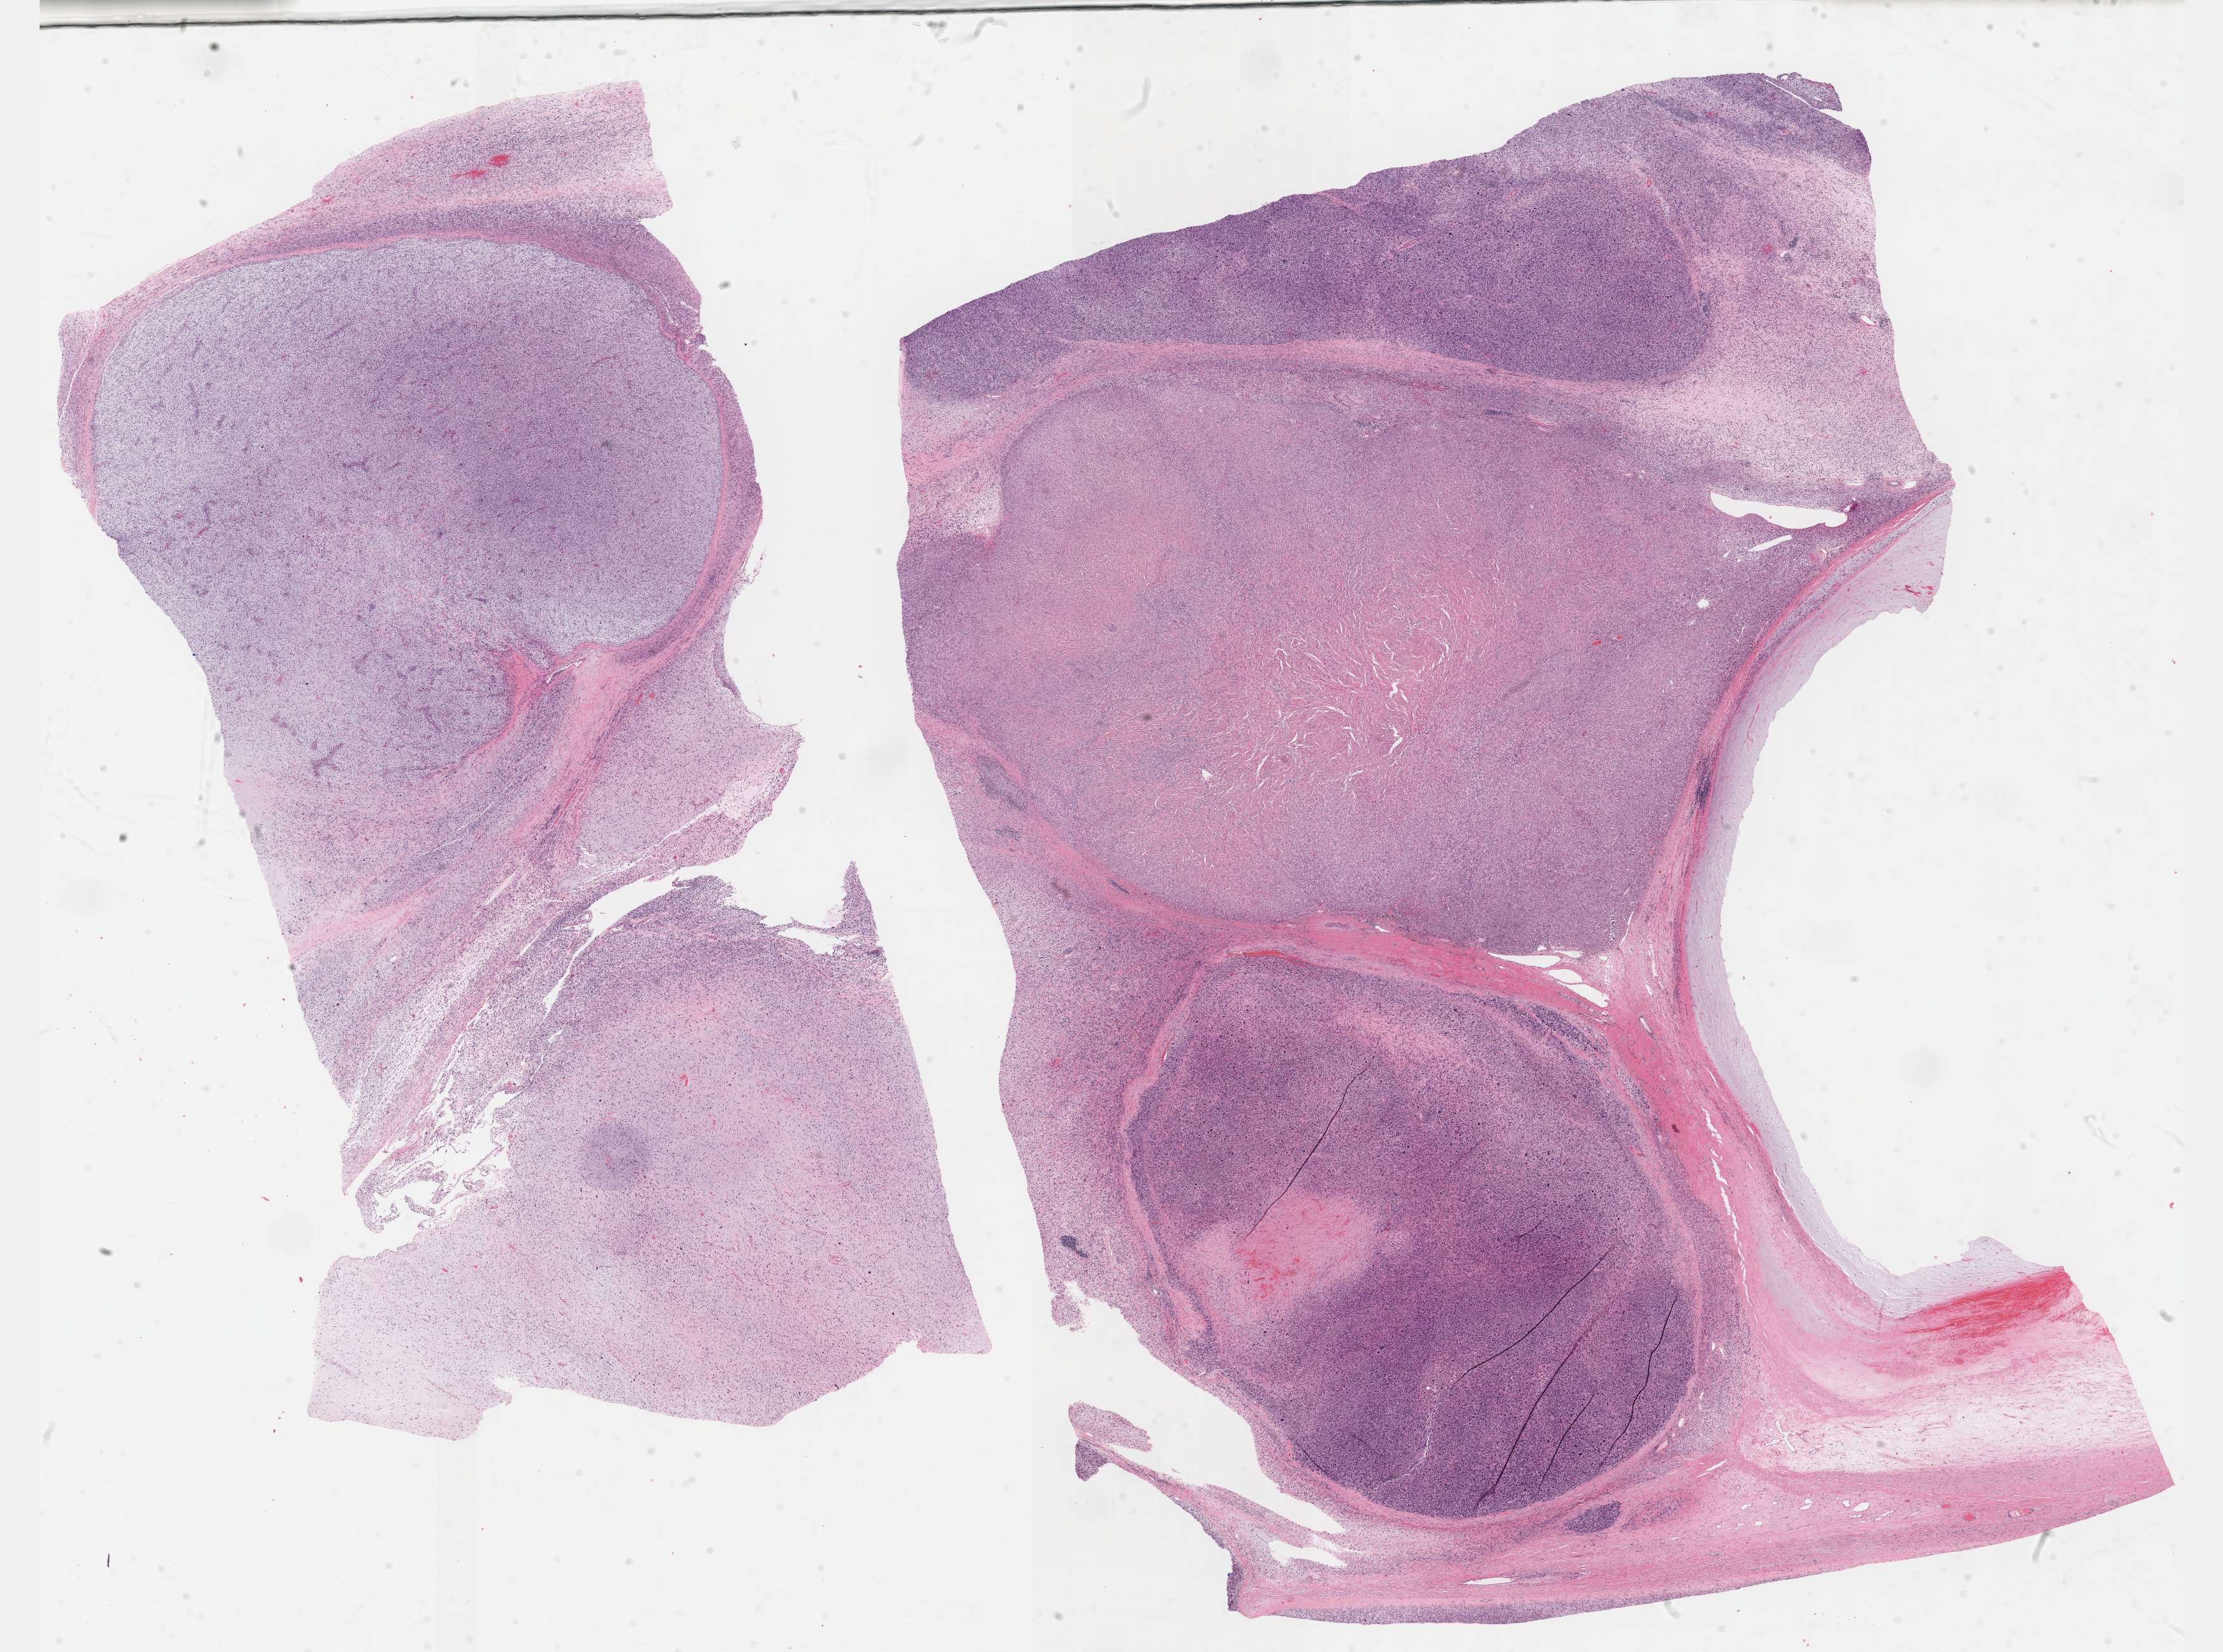
Whole-slide histology image, H&E — low-resolution overview of the scanned area, about 28.2 x 20.9 mm (slide scanned at 40x); formalin-fixed paraffin-embedded (FFPE) diagnostic section; sample: primary tumour, connective, subcutaneous and other soft tissues. Male patient.
Pathologic diagnosis: Fibromyxosarcoma.